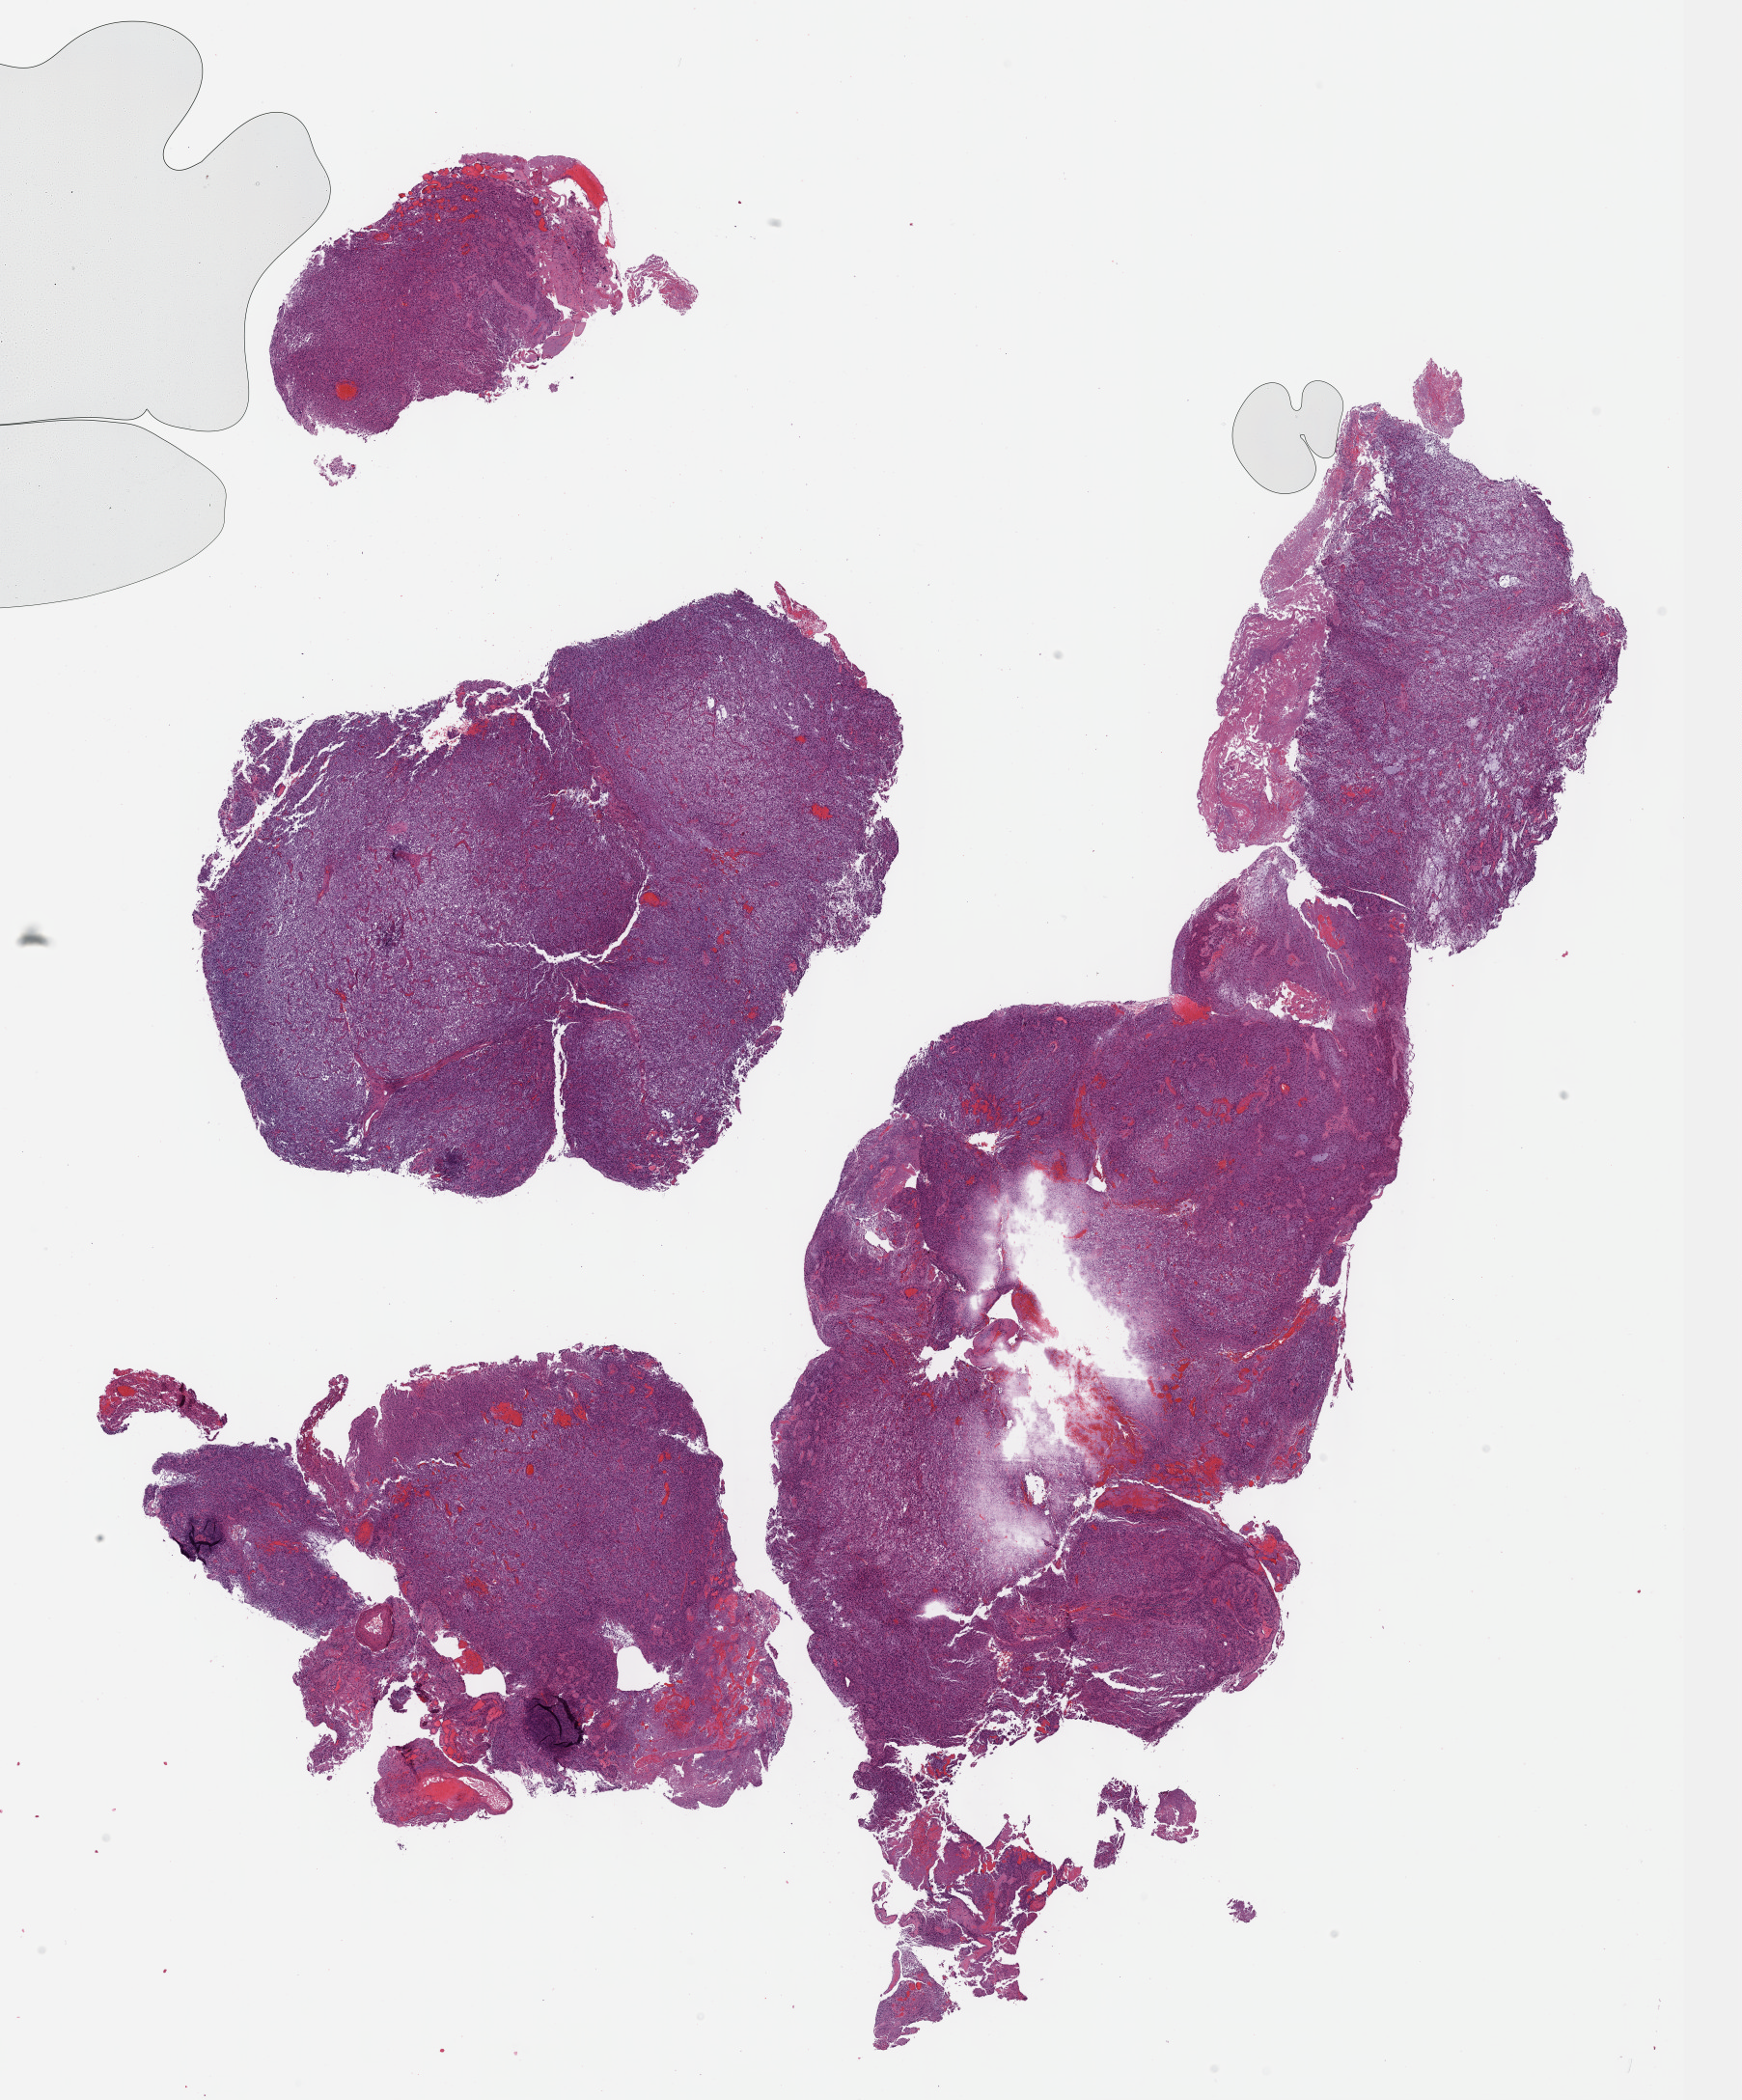
Digitized Hematoxylin and eosin (H&E) stained tissue section (whole slide) — low-resolution overview of the scanned area, about 14.6 x 17.6 mm; formalin-fixed paraffin-embedded (FFPE) diagnostic section; brain, primary tumour sample. Male, age 66 years at initial diagnosis.
Diagnosis: Oligodendroglioma, anaplastic.